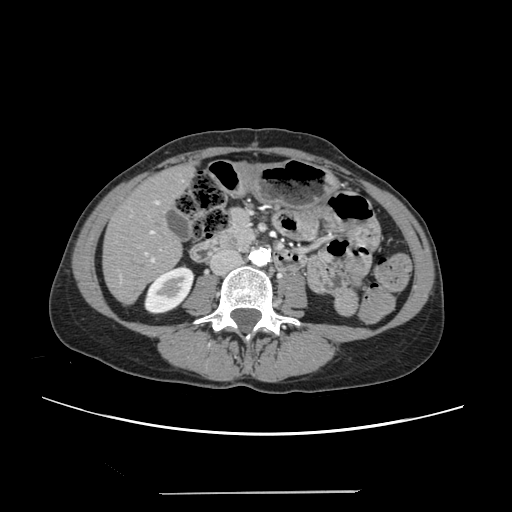
Contrast-enhanced abdominal CT, one axial slice; position 75 of 240 along the scan axis; intravenous contrast given; soft-tissue window (W 400 / L 40 HU); 512 × 512 image matrix, field of view 371 × 371 mm. Female patient, age 60 years. Case-level facts recorded for this patient, not image findings: diagnosis: colorectal cancer liver metastases, imaged before liver resection; multiple liver metastases: no; largest metastasis: 1.5 cm; disease in both lobes: no.
Annotated regions visible in this slice (outlined manually by an expert reader):
- liver: bounding box <105,166,193,303> (left, top, right, bottom; pixels)
- planned liver remnant (the part of the liver to remain after resection): <105,172,181,303>
- portal vein (with intrahepatic branches): <131,200,161,261>